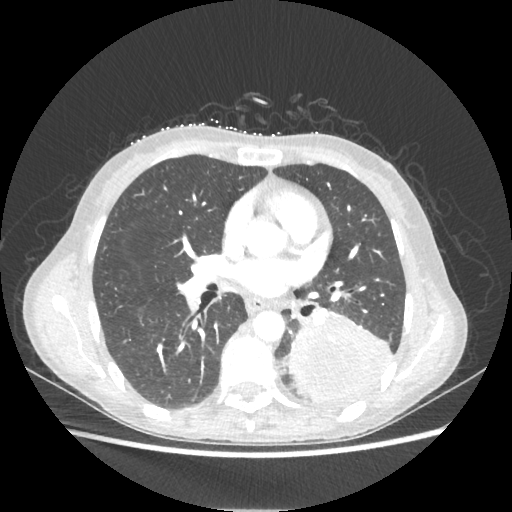
Chest CT, one axial slice; slice 113 of 221 in the series (ordered by position); 80 kVp; lung window (W 1500 / L -600 HU); 1.25 mm slice thickness; 512 × 512 image matrix, field of view 360 × 360 mm. Patient: female, 53 years. Case-level facts recorded for this patient, not image findings: clinical TNM (as recorded): T3 N0 M0.
Annotated regions visible in this slice (rectangle marked by the reading radiologist):
- lung tumour (recorded histology: adenocarcinoma): box from (x=287, y=311) to (x=391, y=405) px